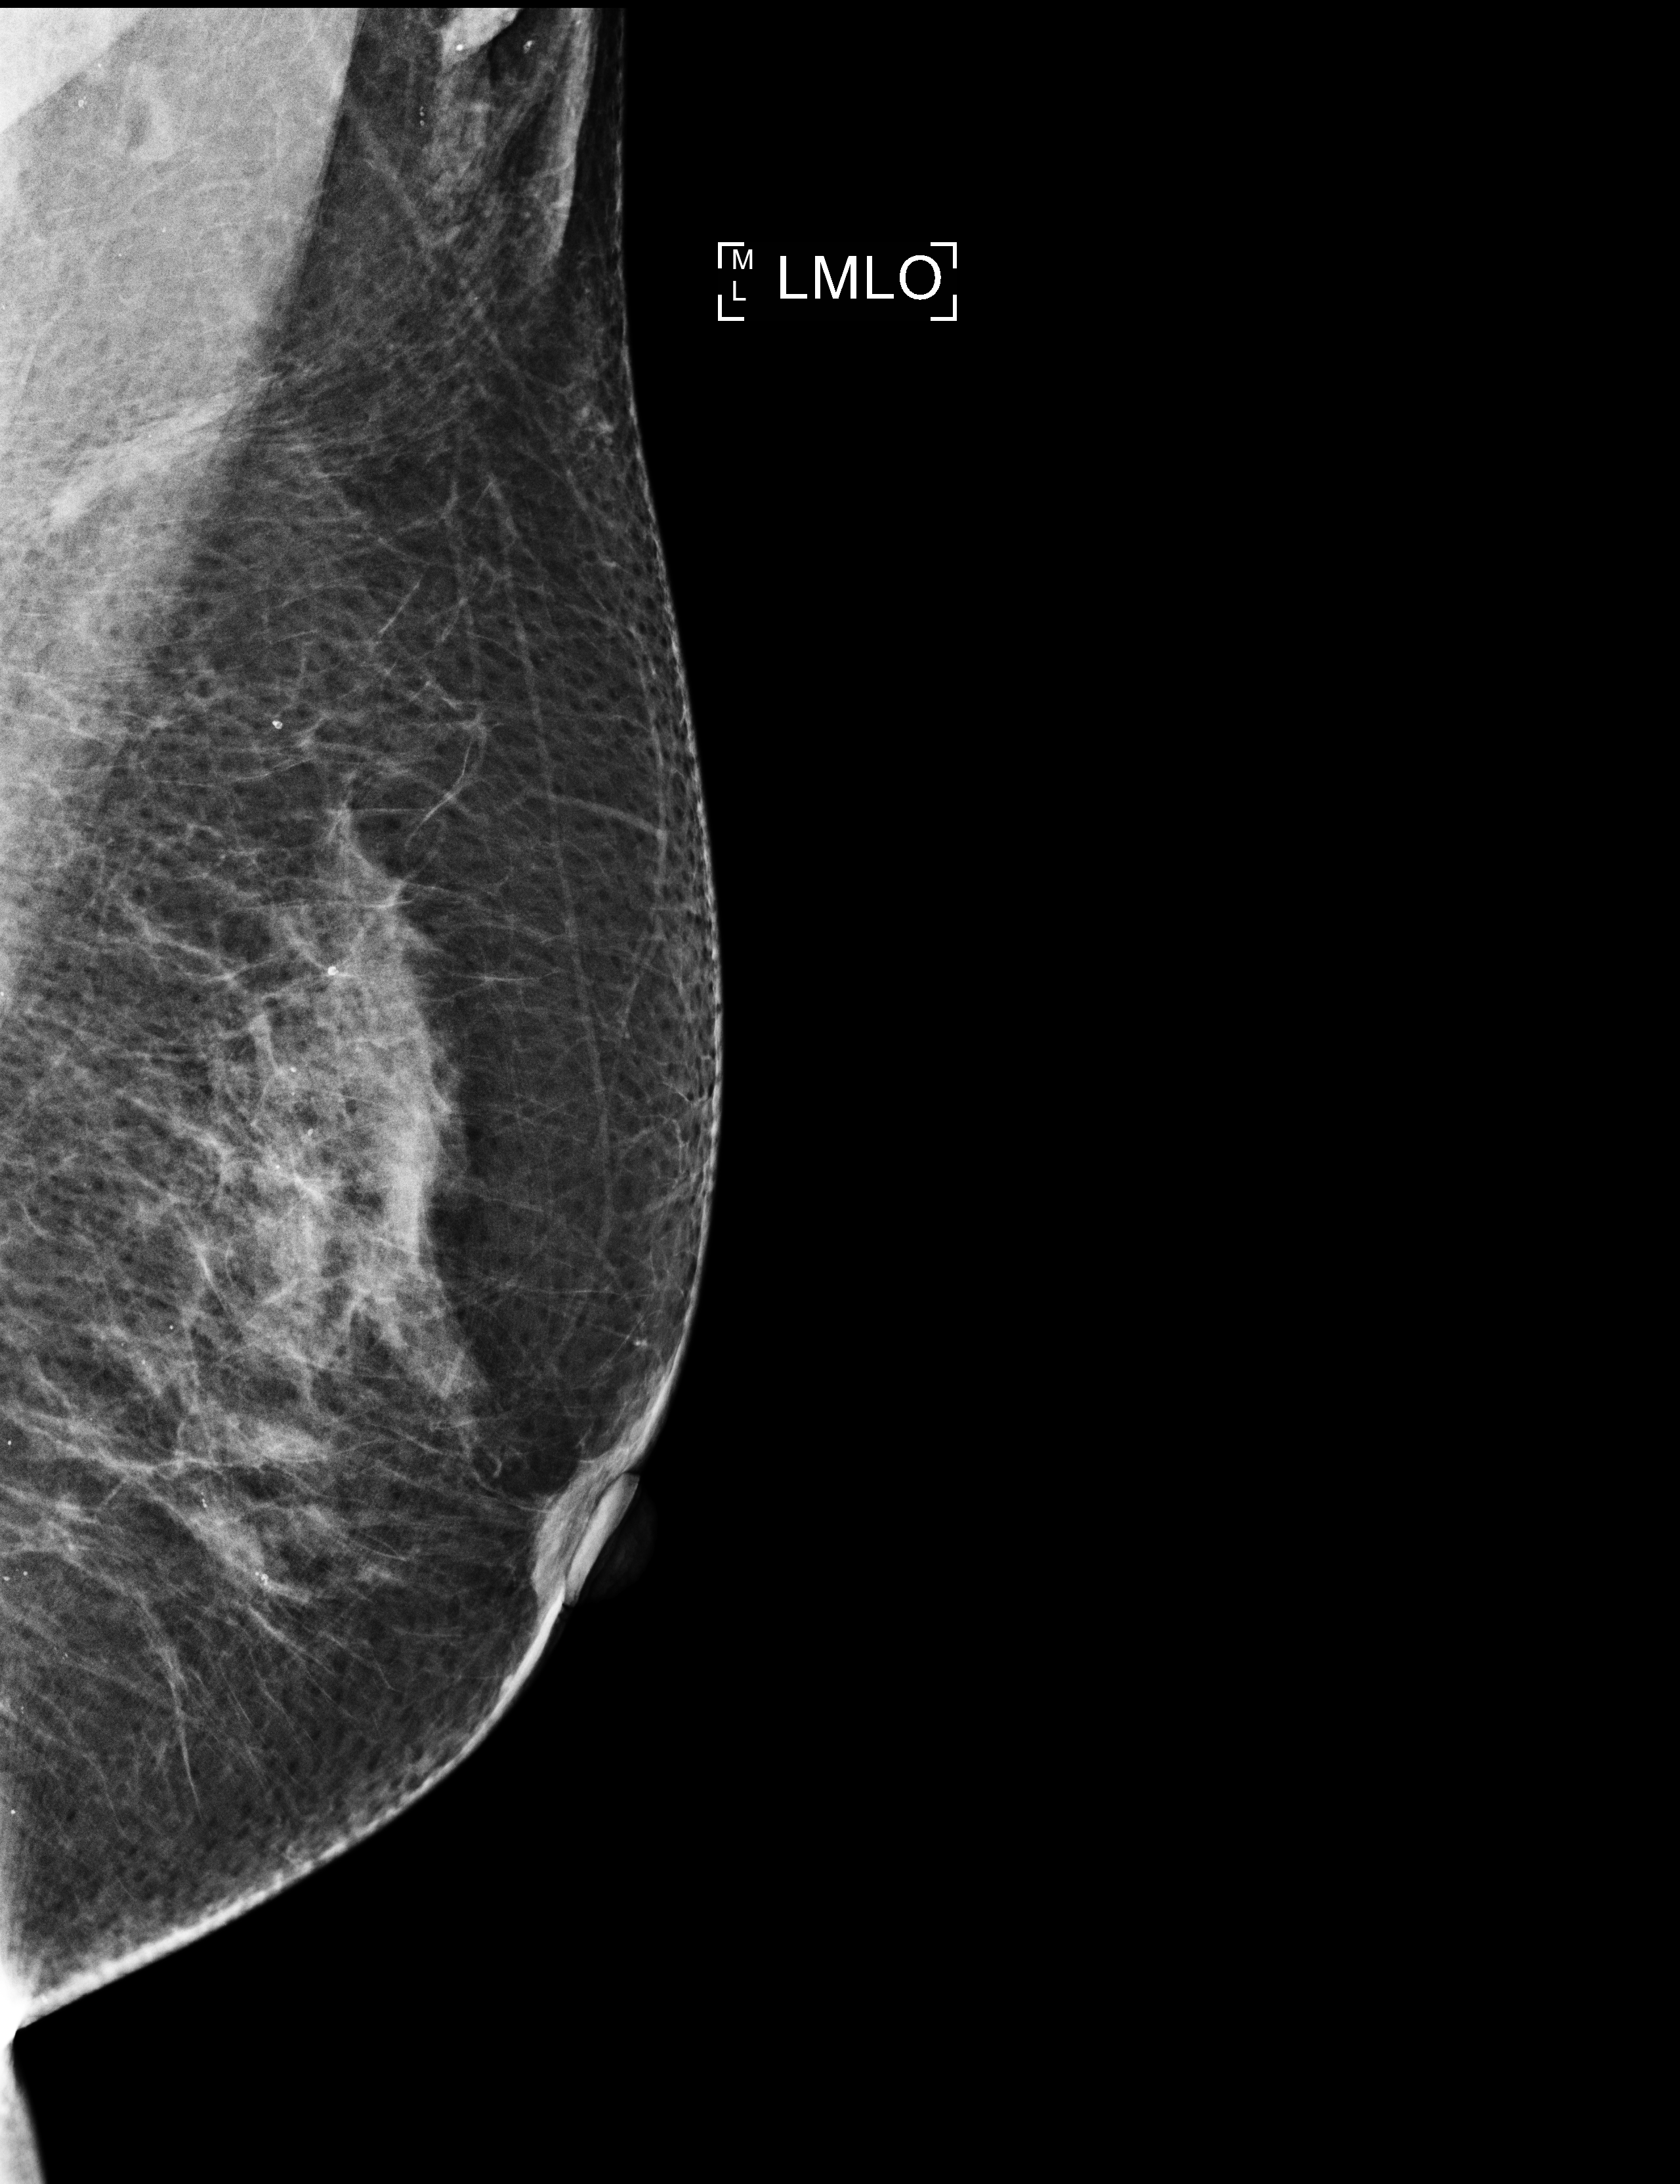
Digital mammogram (FFDM), left breast, mediolateral oblique (MLO) view, annual screening mammography examination, compressed breast thickness 63 mm, system: Selenia Dimensions. Patient: female, 68 years.
Breast density at the screening exam (both breasts): heterogeneously dense (BI-RADS density category c). Final BI-RADS category for the screening round (tomosynthesis exam, both breasts): category 2. Recall: no recall after this screen.